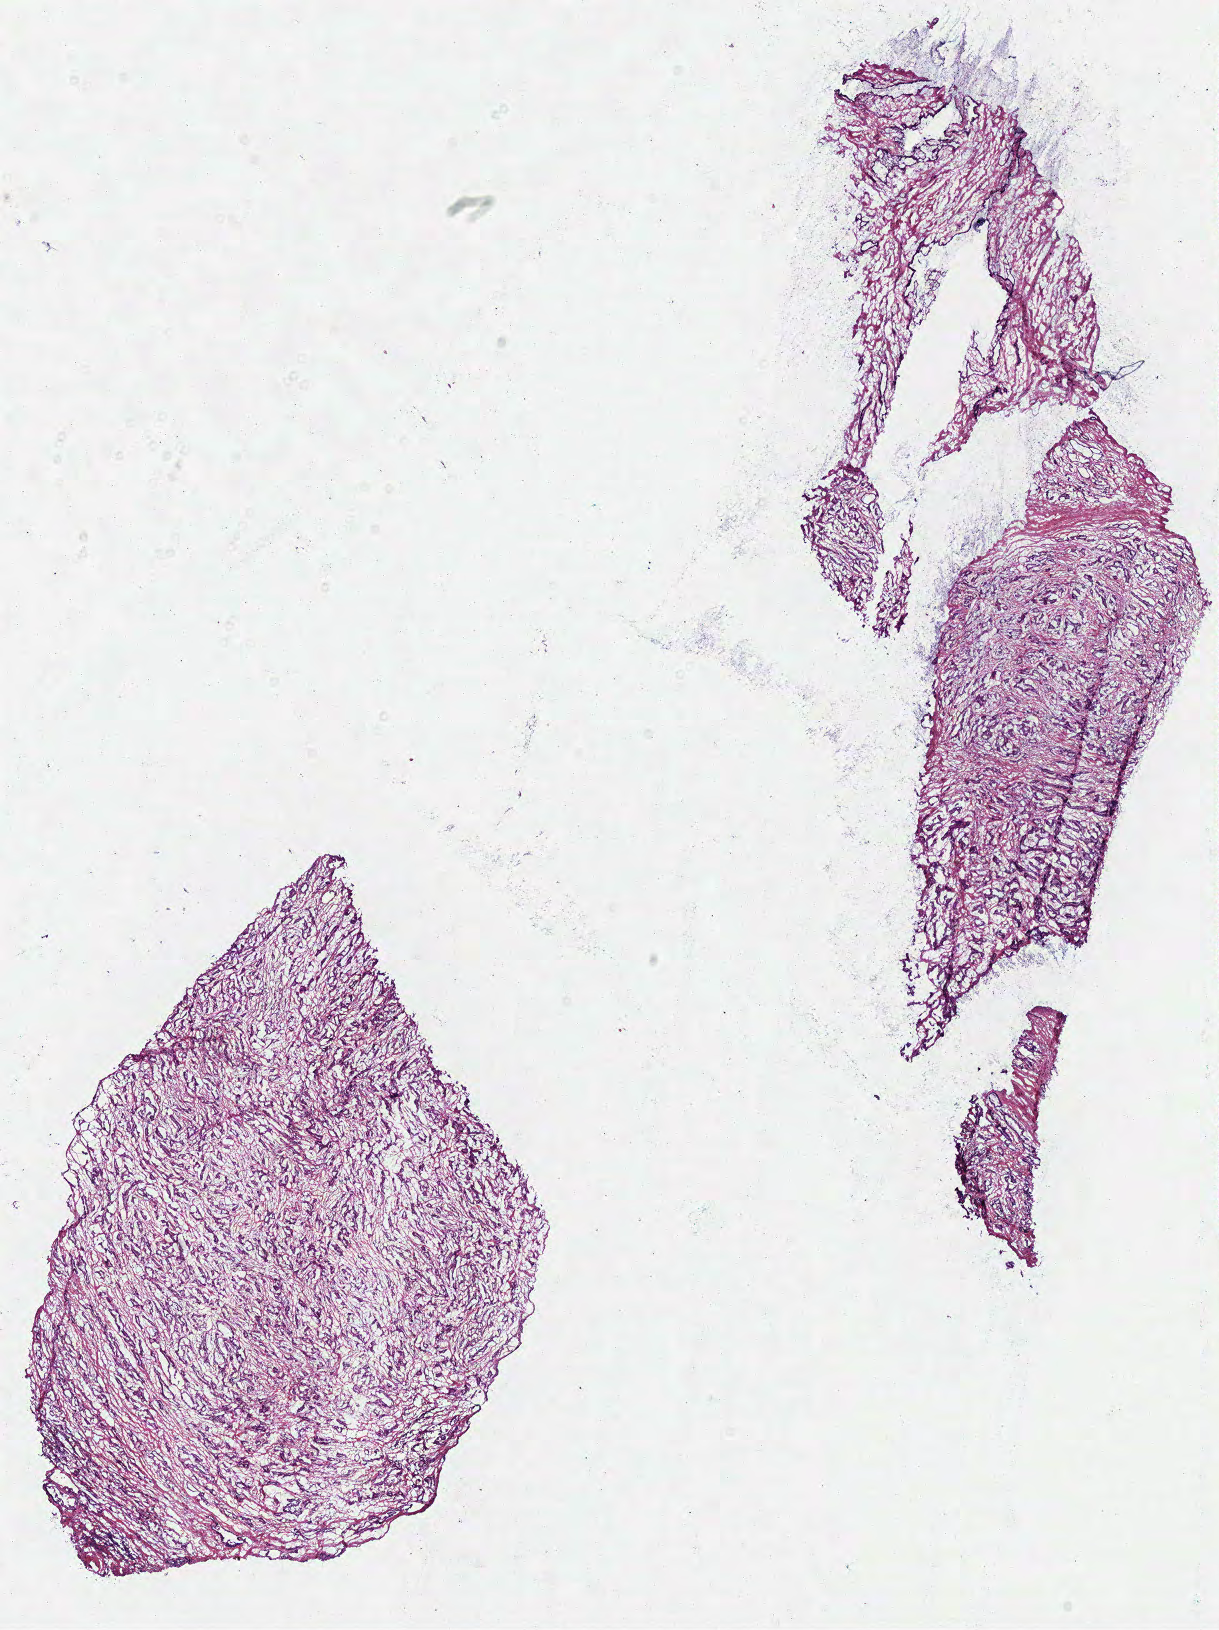
Digitized H&E tissue section (whole slide), a low-resolution overview of the entire scanned area, about 9.6 x 12.8 mm (from a 40x scan), frozen section from the top of the tissue portion, prostate, primary tumour sample. Patient: male, age at initial diagnosis 58 years. Gleason score: 6 (3+3). Pathologist review of this section (percent, as recorded): tumour cells 60%, tumour nuclei 70%, normal cells 0%, stromal cells 40%, necrosis 0%.
• pathologic diagnosis: Acinar cell carcinoma (prostate gland)
• lymph nodes positive (case pathology): 0 of 6 examined
• laterality: bilateral